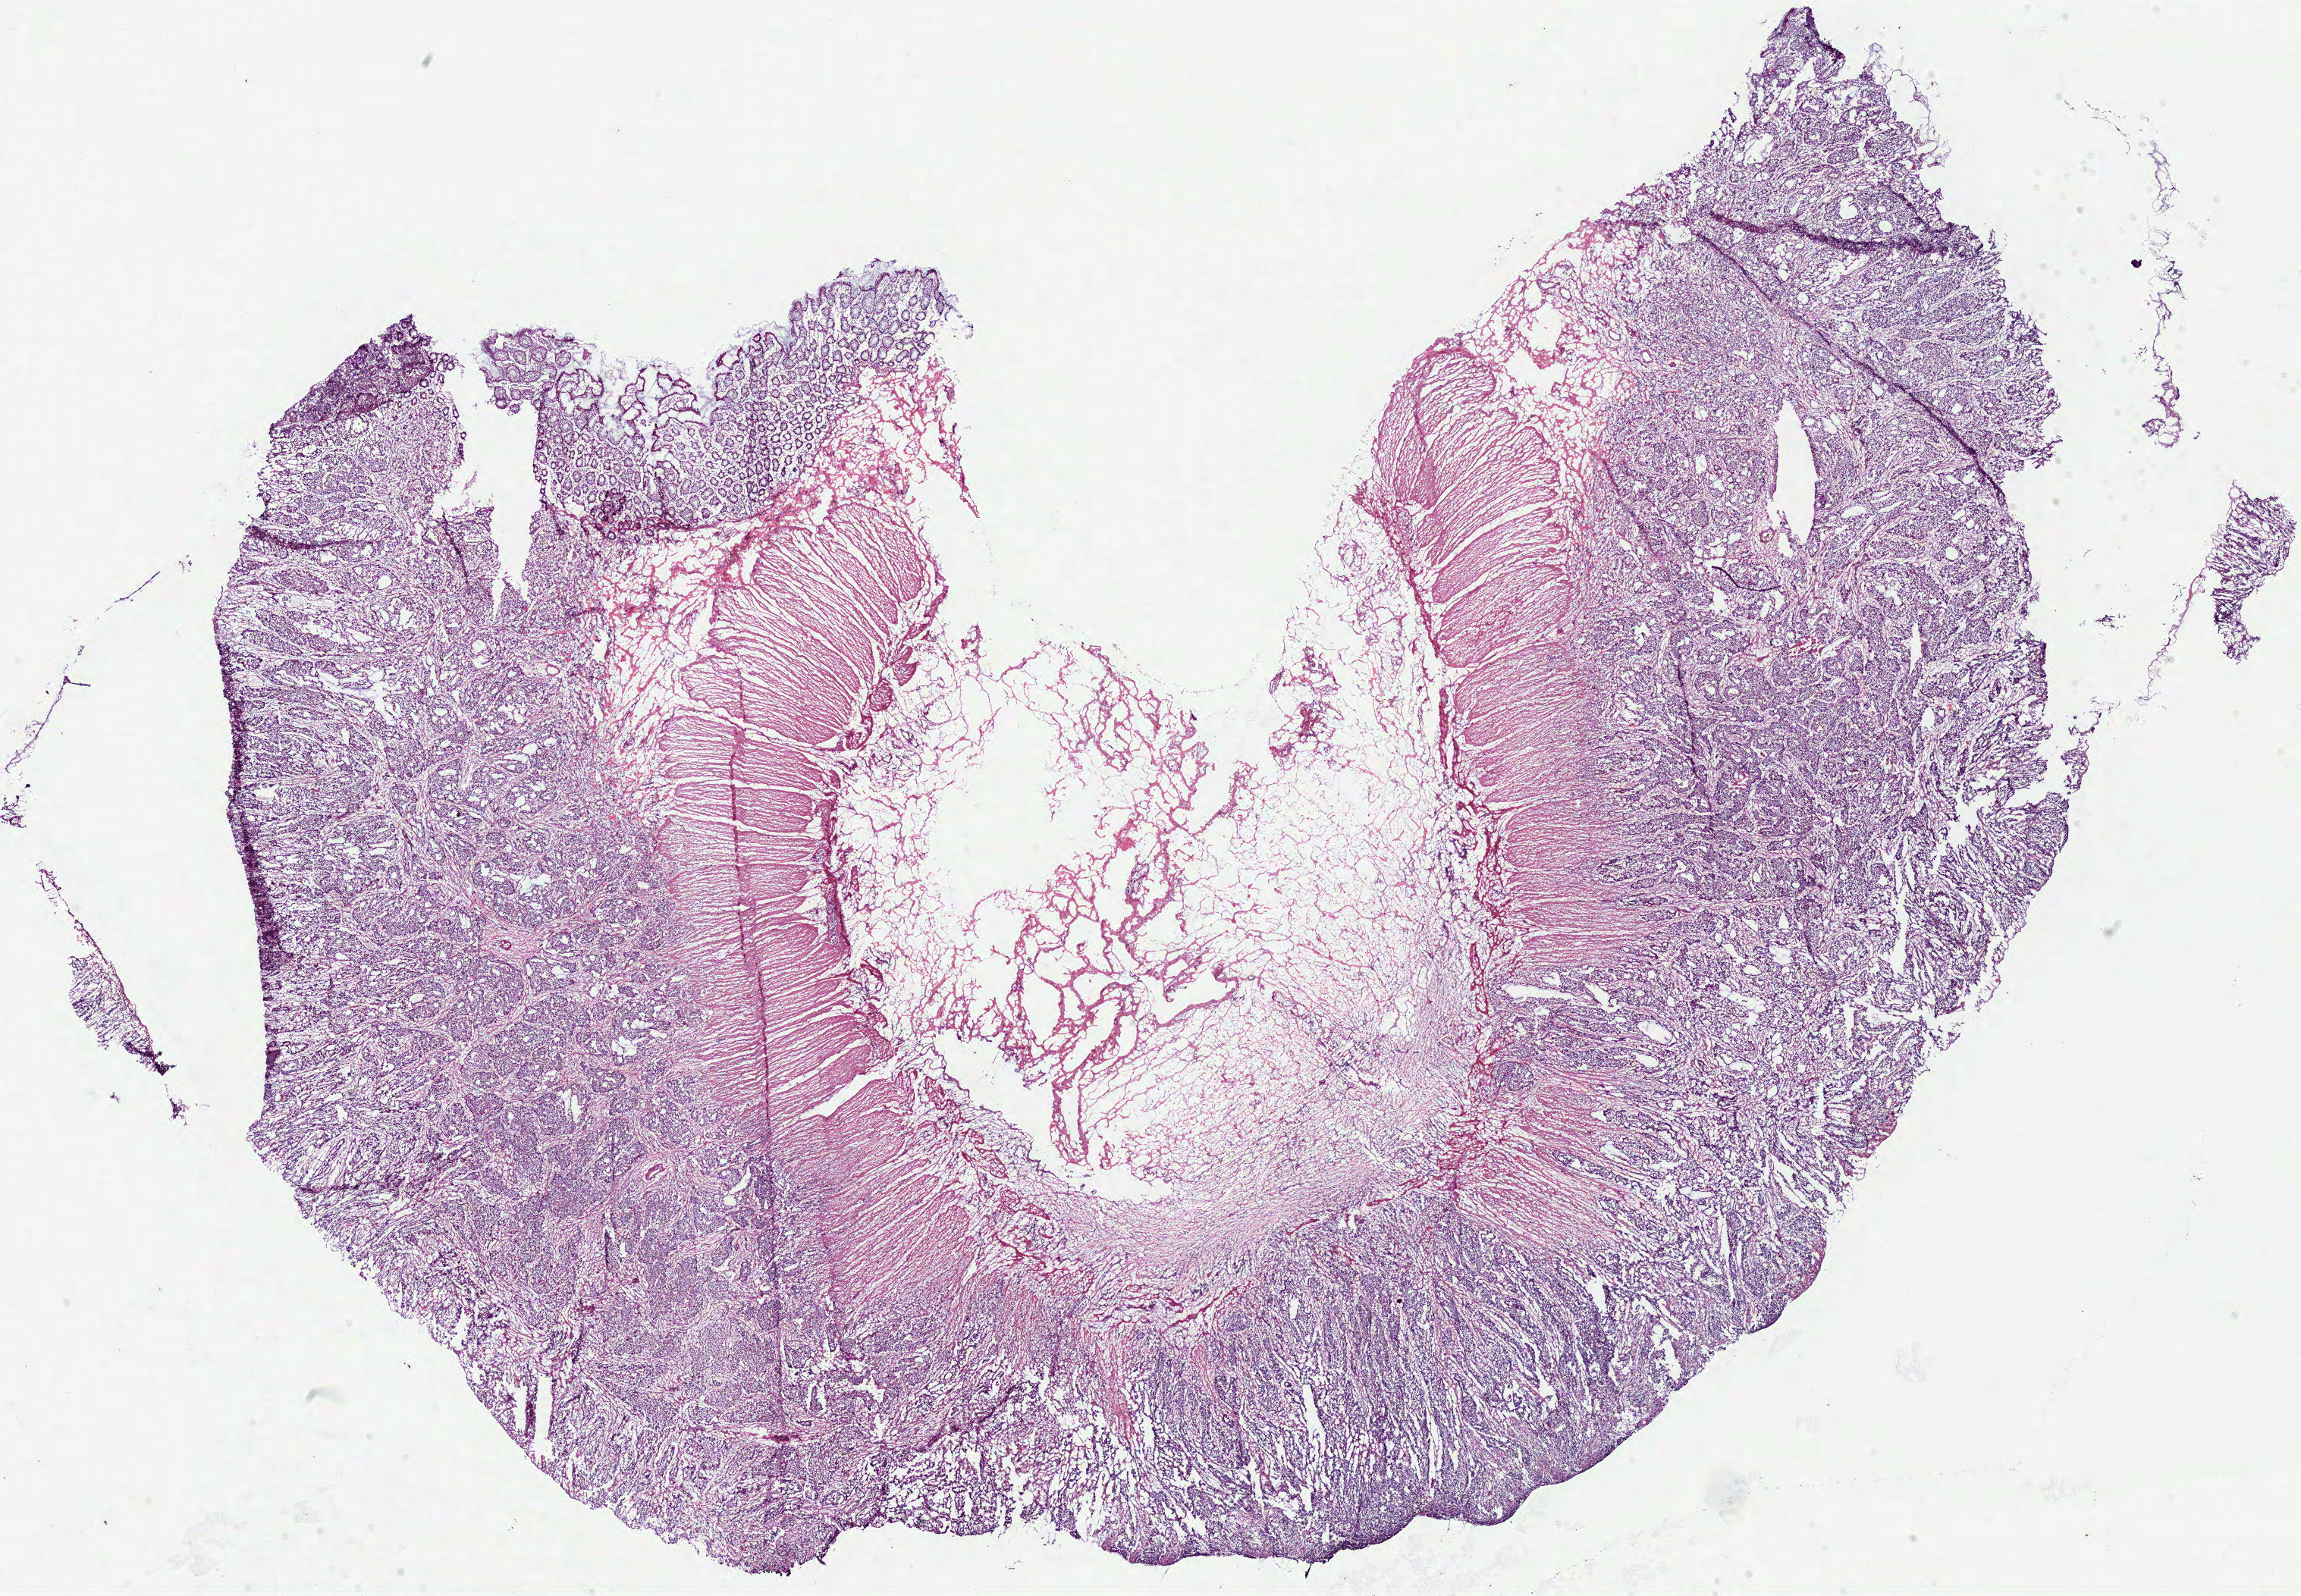
Digitized H&E-stained tissue section (whole slide) — a low-resolution overview of the entire scanned area, about 23.9 x 16.6 mm; frozen section from the bottom of the tissue portion; sample: primary tumour, colon. Female, age 58 years at initial diagnosis. Composition of this section per pathologist review: tumour cells 55%, tumour nuclei 80%, normal cells 10%, stromal cells 30%, necrosis 5%.
AJCC pathologic stage: IIA. Histologic diagnosis: Adenocarcinoma, NOS.